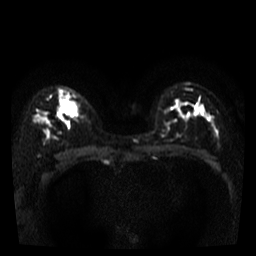
Breast MRI, one axial slice; position 25 of 40 along the scan axis; diffusion-weighted series; image 2 of 4 stored at this slice position (different b-values; order by instance number); 3 T; 5 mm slice thickness; 256 × 256 image matrix, field of view 280 × 280 mm. Female patient.
Structures marked on this image (expert manual segmentation):
- tumour on diffusion-weighted imaging: bounding box [x1, y1, x2, y2] px = [62, 103, 77, 115]